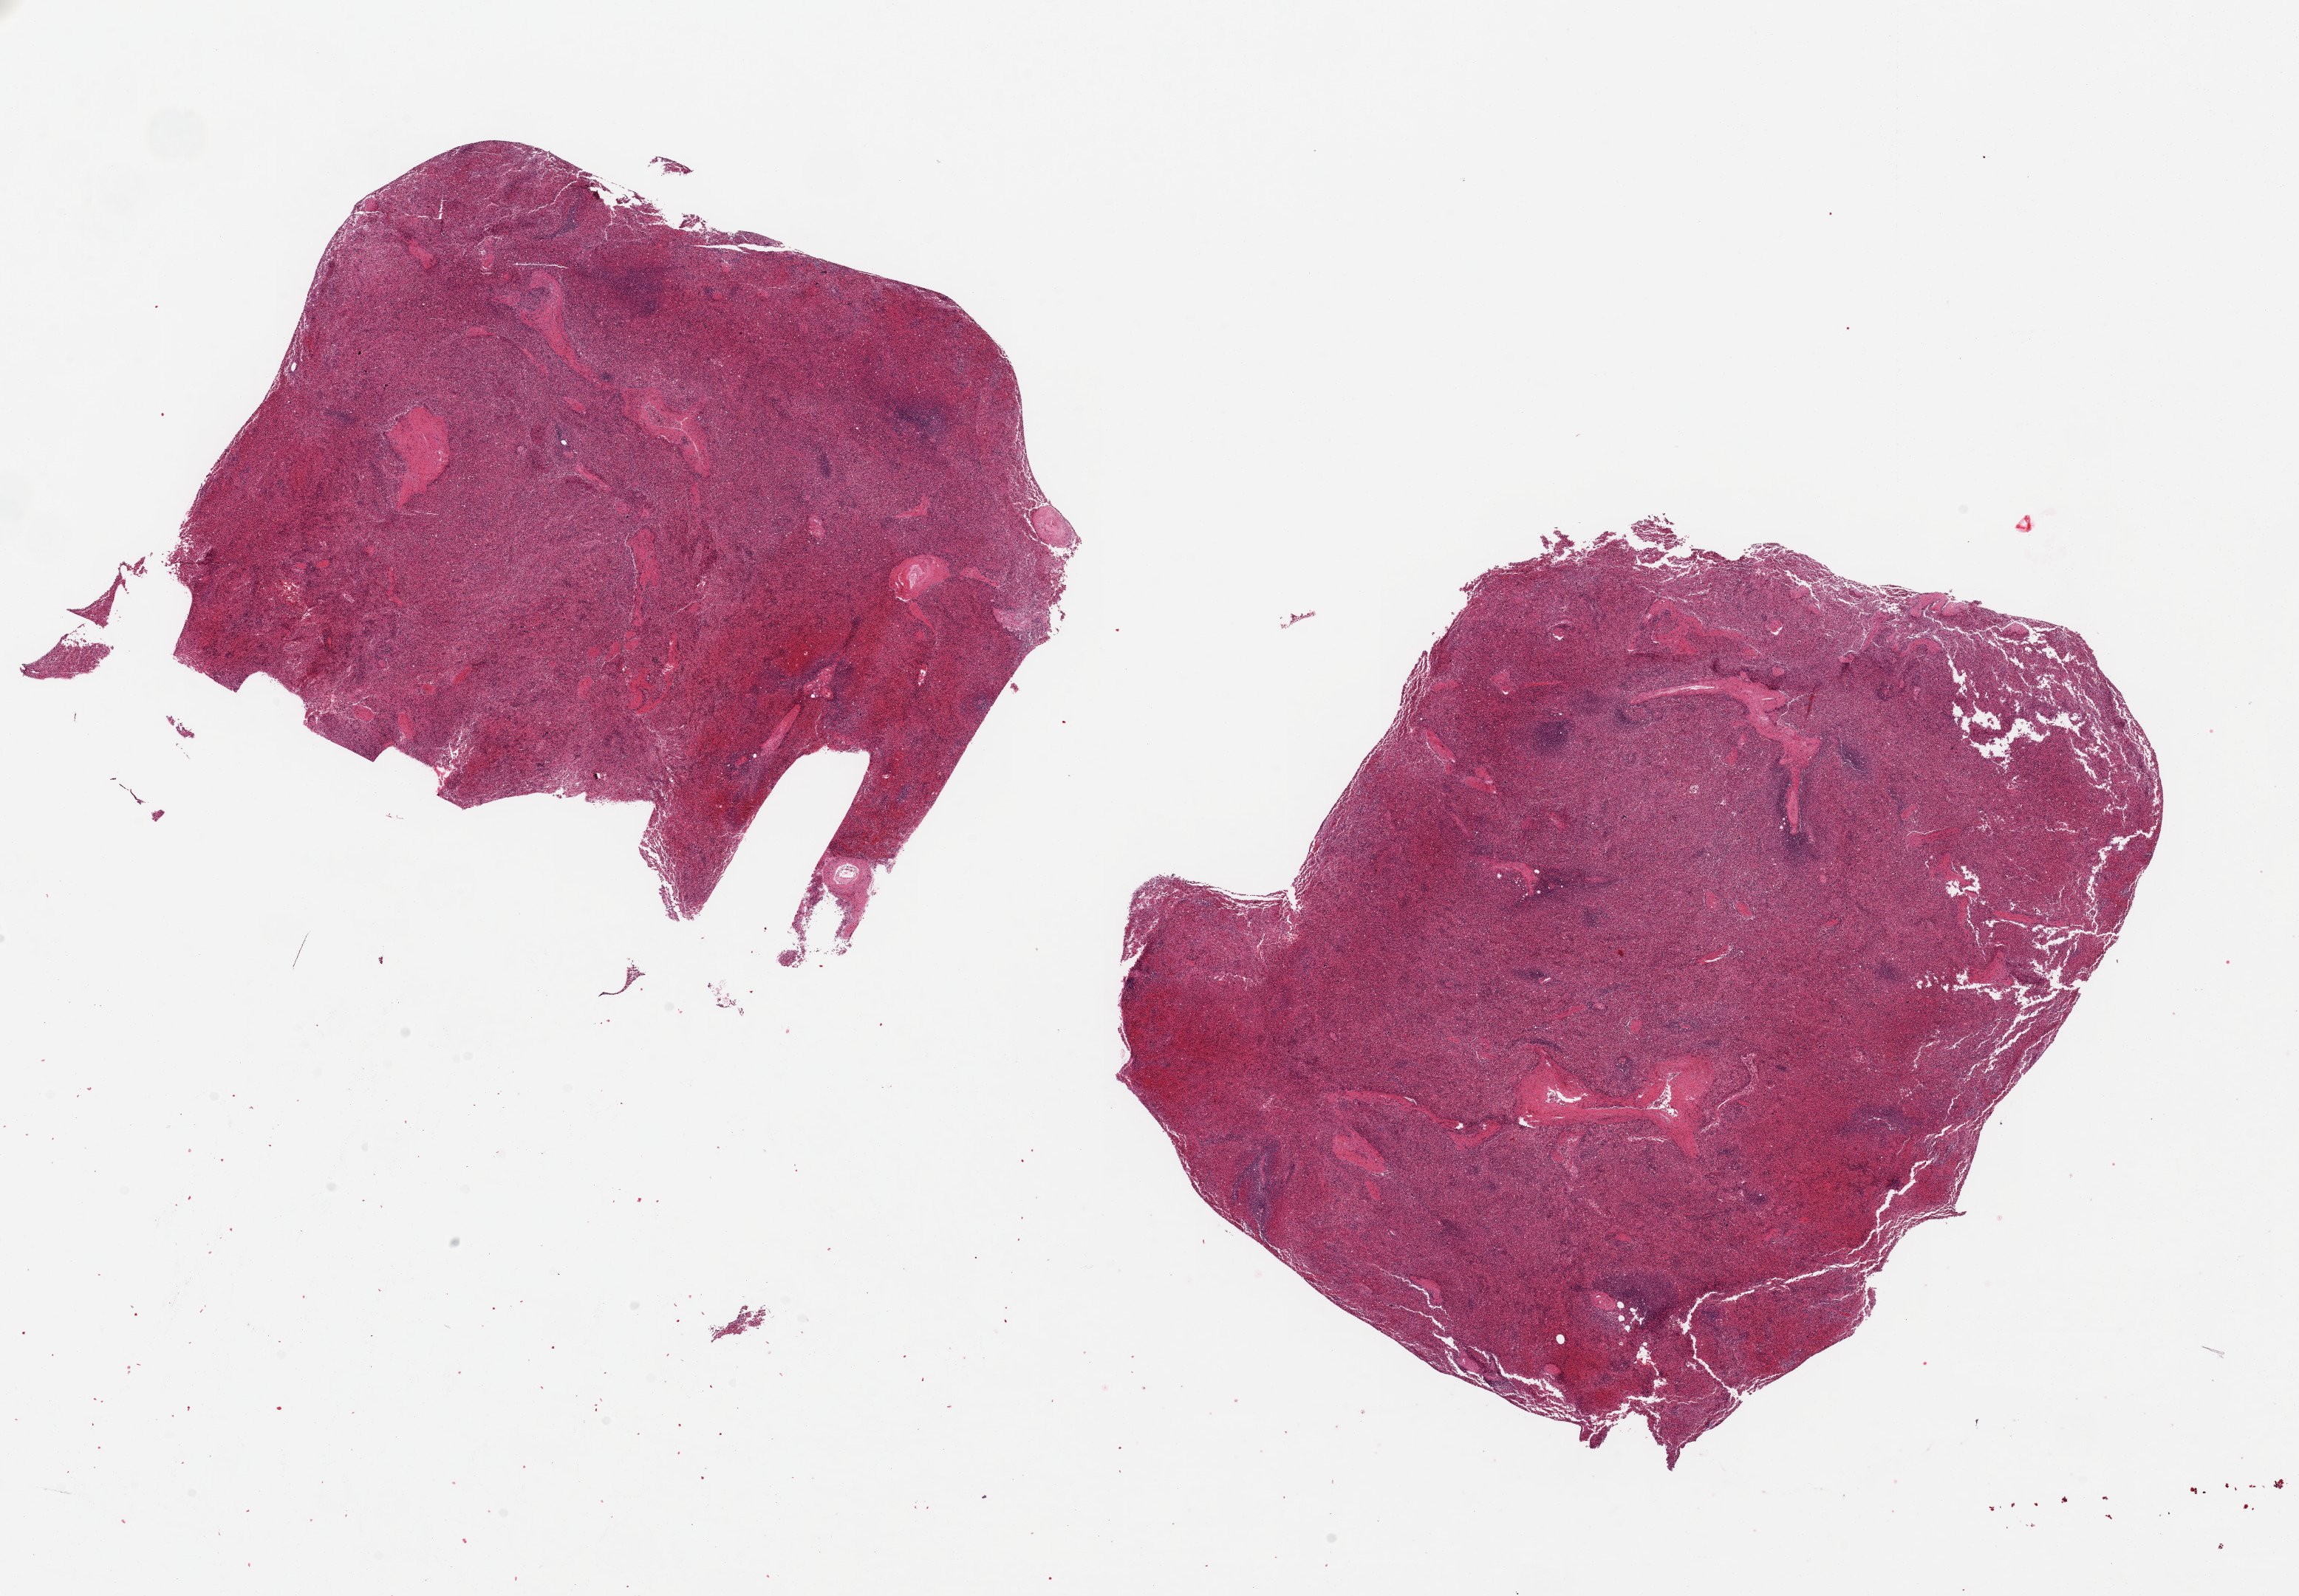
Digitized H&E-stained section, brightfield — a low-resolution overview of the entire scanned area, about 24.6 x 17.1 mm (from a 20x scan). PAXgene-fixed paraffin-embedded (PFPE) section. Target tissue: spleen. Donor tissue sample. Donor sex: female.
* reviewer comment on this tissue sample: 2 ~8.5x6.5mm aliquots, areas of poor/under-fixation